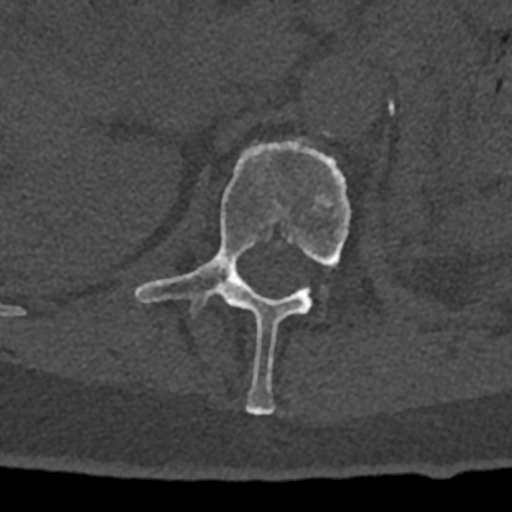
CT including the spine, one axial slice. Position 430 of 797 along the scan axis. Reconstruction kernel Br40s/3. Bone window (W 1800 / L 400 HU). 0.5 mm slice thickness. 512 × 512 image matrix, field of view 160 × 160 mm. Male patient, age 74 years. From the clinical record (not read from this slice): primary cancer: renal.
Structures marked on this image (semi-automatically segmented with operator editing):
- L1 vertebra: bounding box (x1, y1, x2, y2) in pixels: (134, 139, 350, 415)